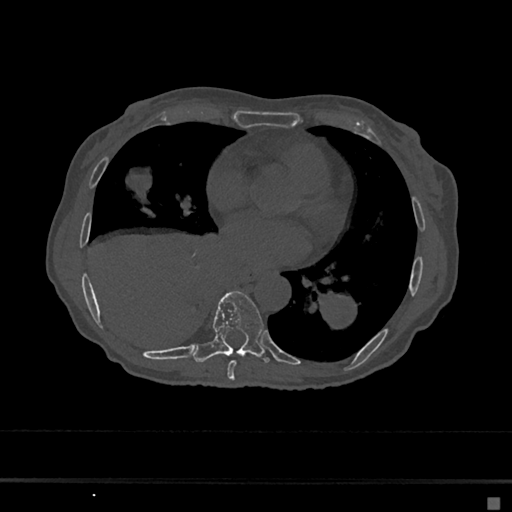
CT including the spine, one axial slice; slice 334 of 797 in the series (ordered by position); bone window (W 1800 / L 400 HU); 0.5 mm slice thickness; 512 × 512 image matrix, field of view 360 × 360 mm. Female patient, age 68 years. Case-level facts recorded for this patient, not image findings: primary cancer: renal.
Outlined on this slice (semi-automatic segmentation, software-assisted and operator-edited):
- T7 vertebra: box from (x=227, y=360) to (x=236, y=380) px
- T8 vertebra: (x=193, y=291)–(x=269, y=363)